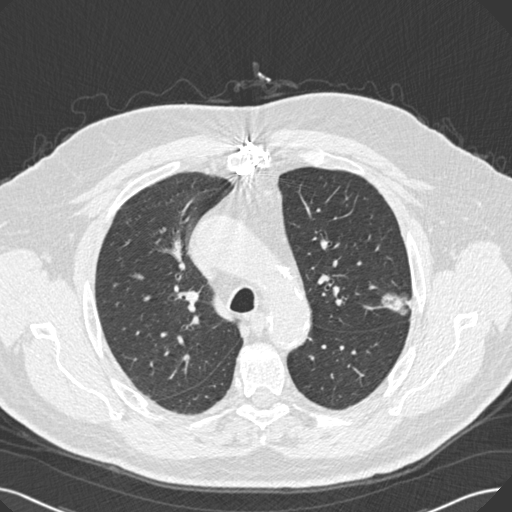
Low-dose screening chest CT, one axial slice. Position 186 of 269 along the scan axis. Reconstruction kernel B30f. 120 kVp. Lung window (W 1500 / L -600 HU). 512 × 512 image matrix, field of view 370 × 370 mm.
Outlined on this slice (expert manual segmentation):
- lesion 1 (tumor, upper lobe of left lung): box from (x=381, y=293) to (x=411, y=315) px